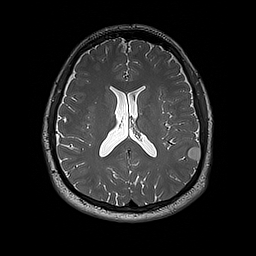
Brain MRI from a brain-tumour surgery series, one axial slice. Position 86 of 192 along the scan axis. 1 mm slice thickness. 256 × 256 image matrix, field of view 250 × 250 mm. Case-level facts recorded for this patient, not image findings: histopathology: Dysembryoplastic neuroepithelial tumor; WHO grade: 1; IDH mutation: no; tumour location: Left Inferior Parietal.
Outlined on this slice (outlined manually by an expert reader):
- tumour: bounding box (x1, y1, x2, y2) in pixels: (188, 147, 201, 162)